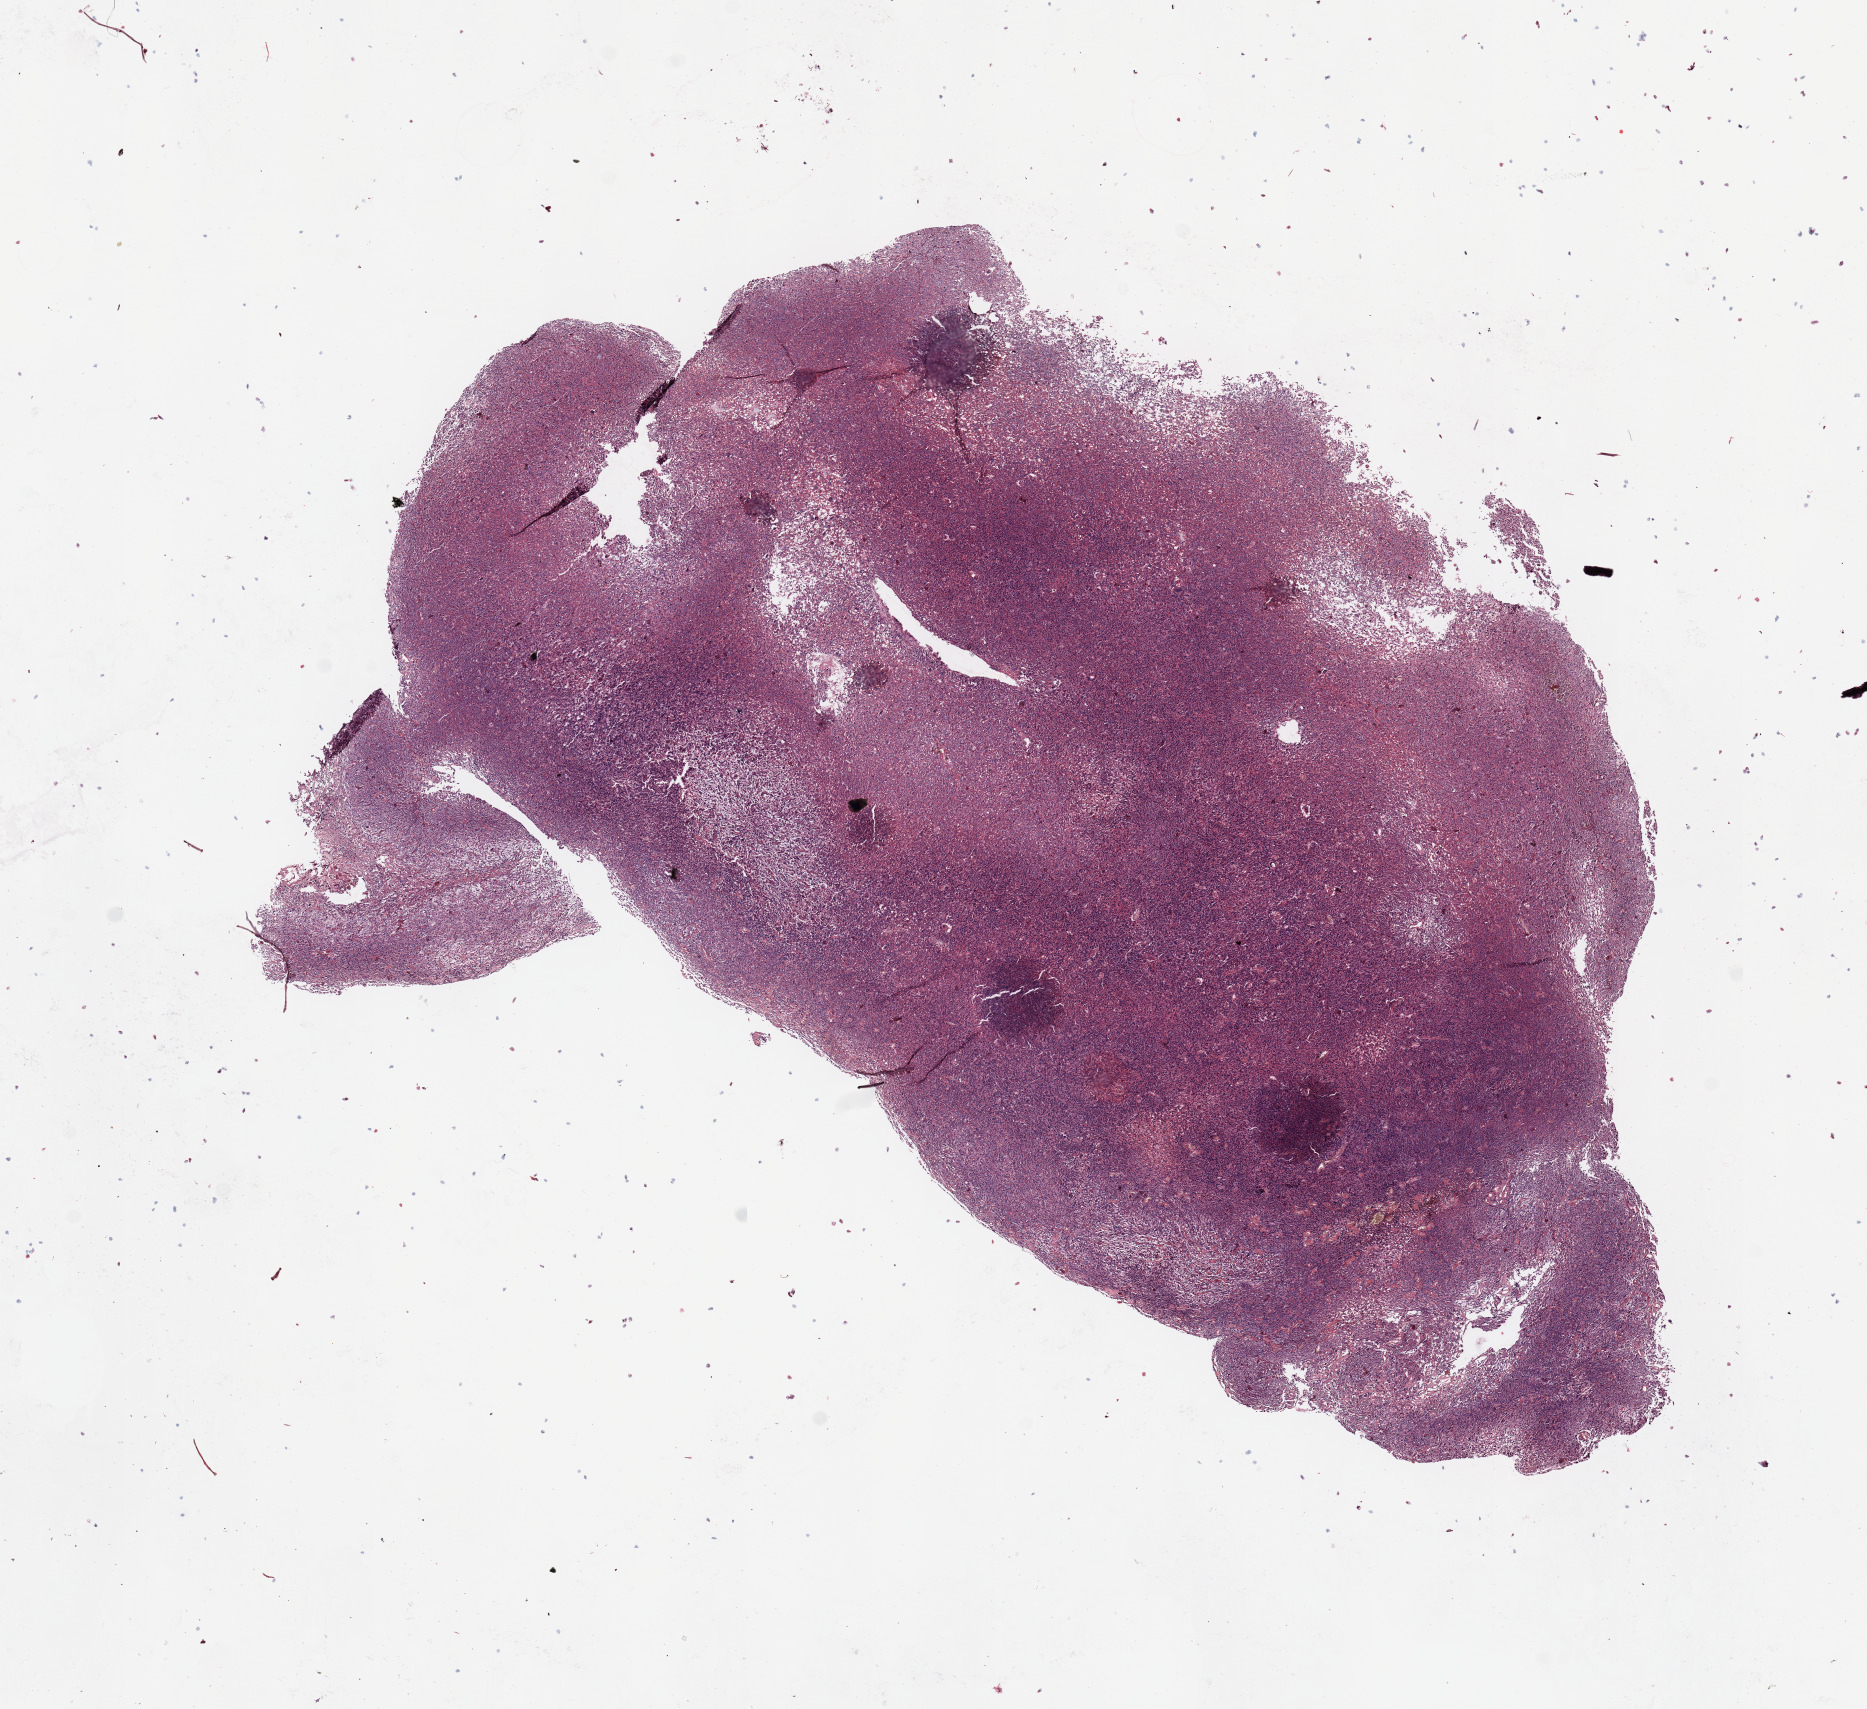
Whole-slide histology image, Hematoxylin and eosin (H&E) stained, whole scanned area (about 14.8 x 13.5 mm, from a 20x scan) shown as a low-resolution overview, tumour tissue sample. Patient: female, age 58 years.
Patient diagnosis (cohort enrolment): sarcoma (site not recorded at cohort level). Primary tumour site (as recorded): upper extremity.